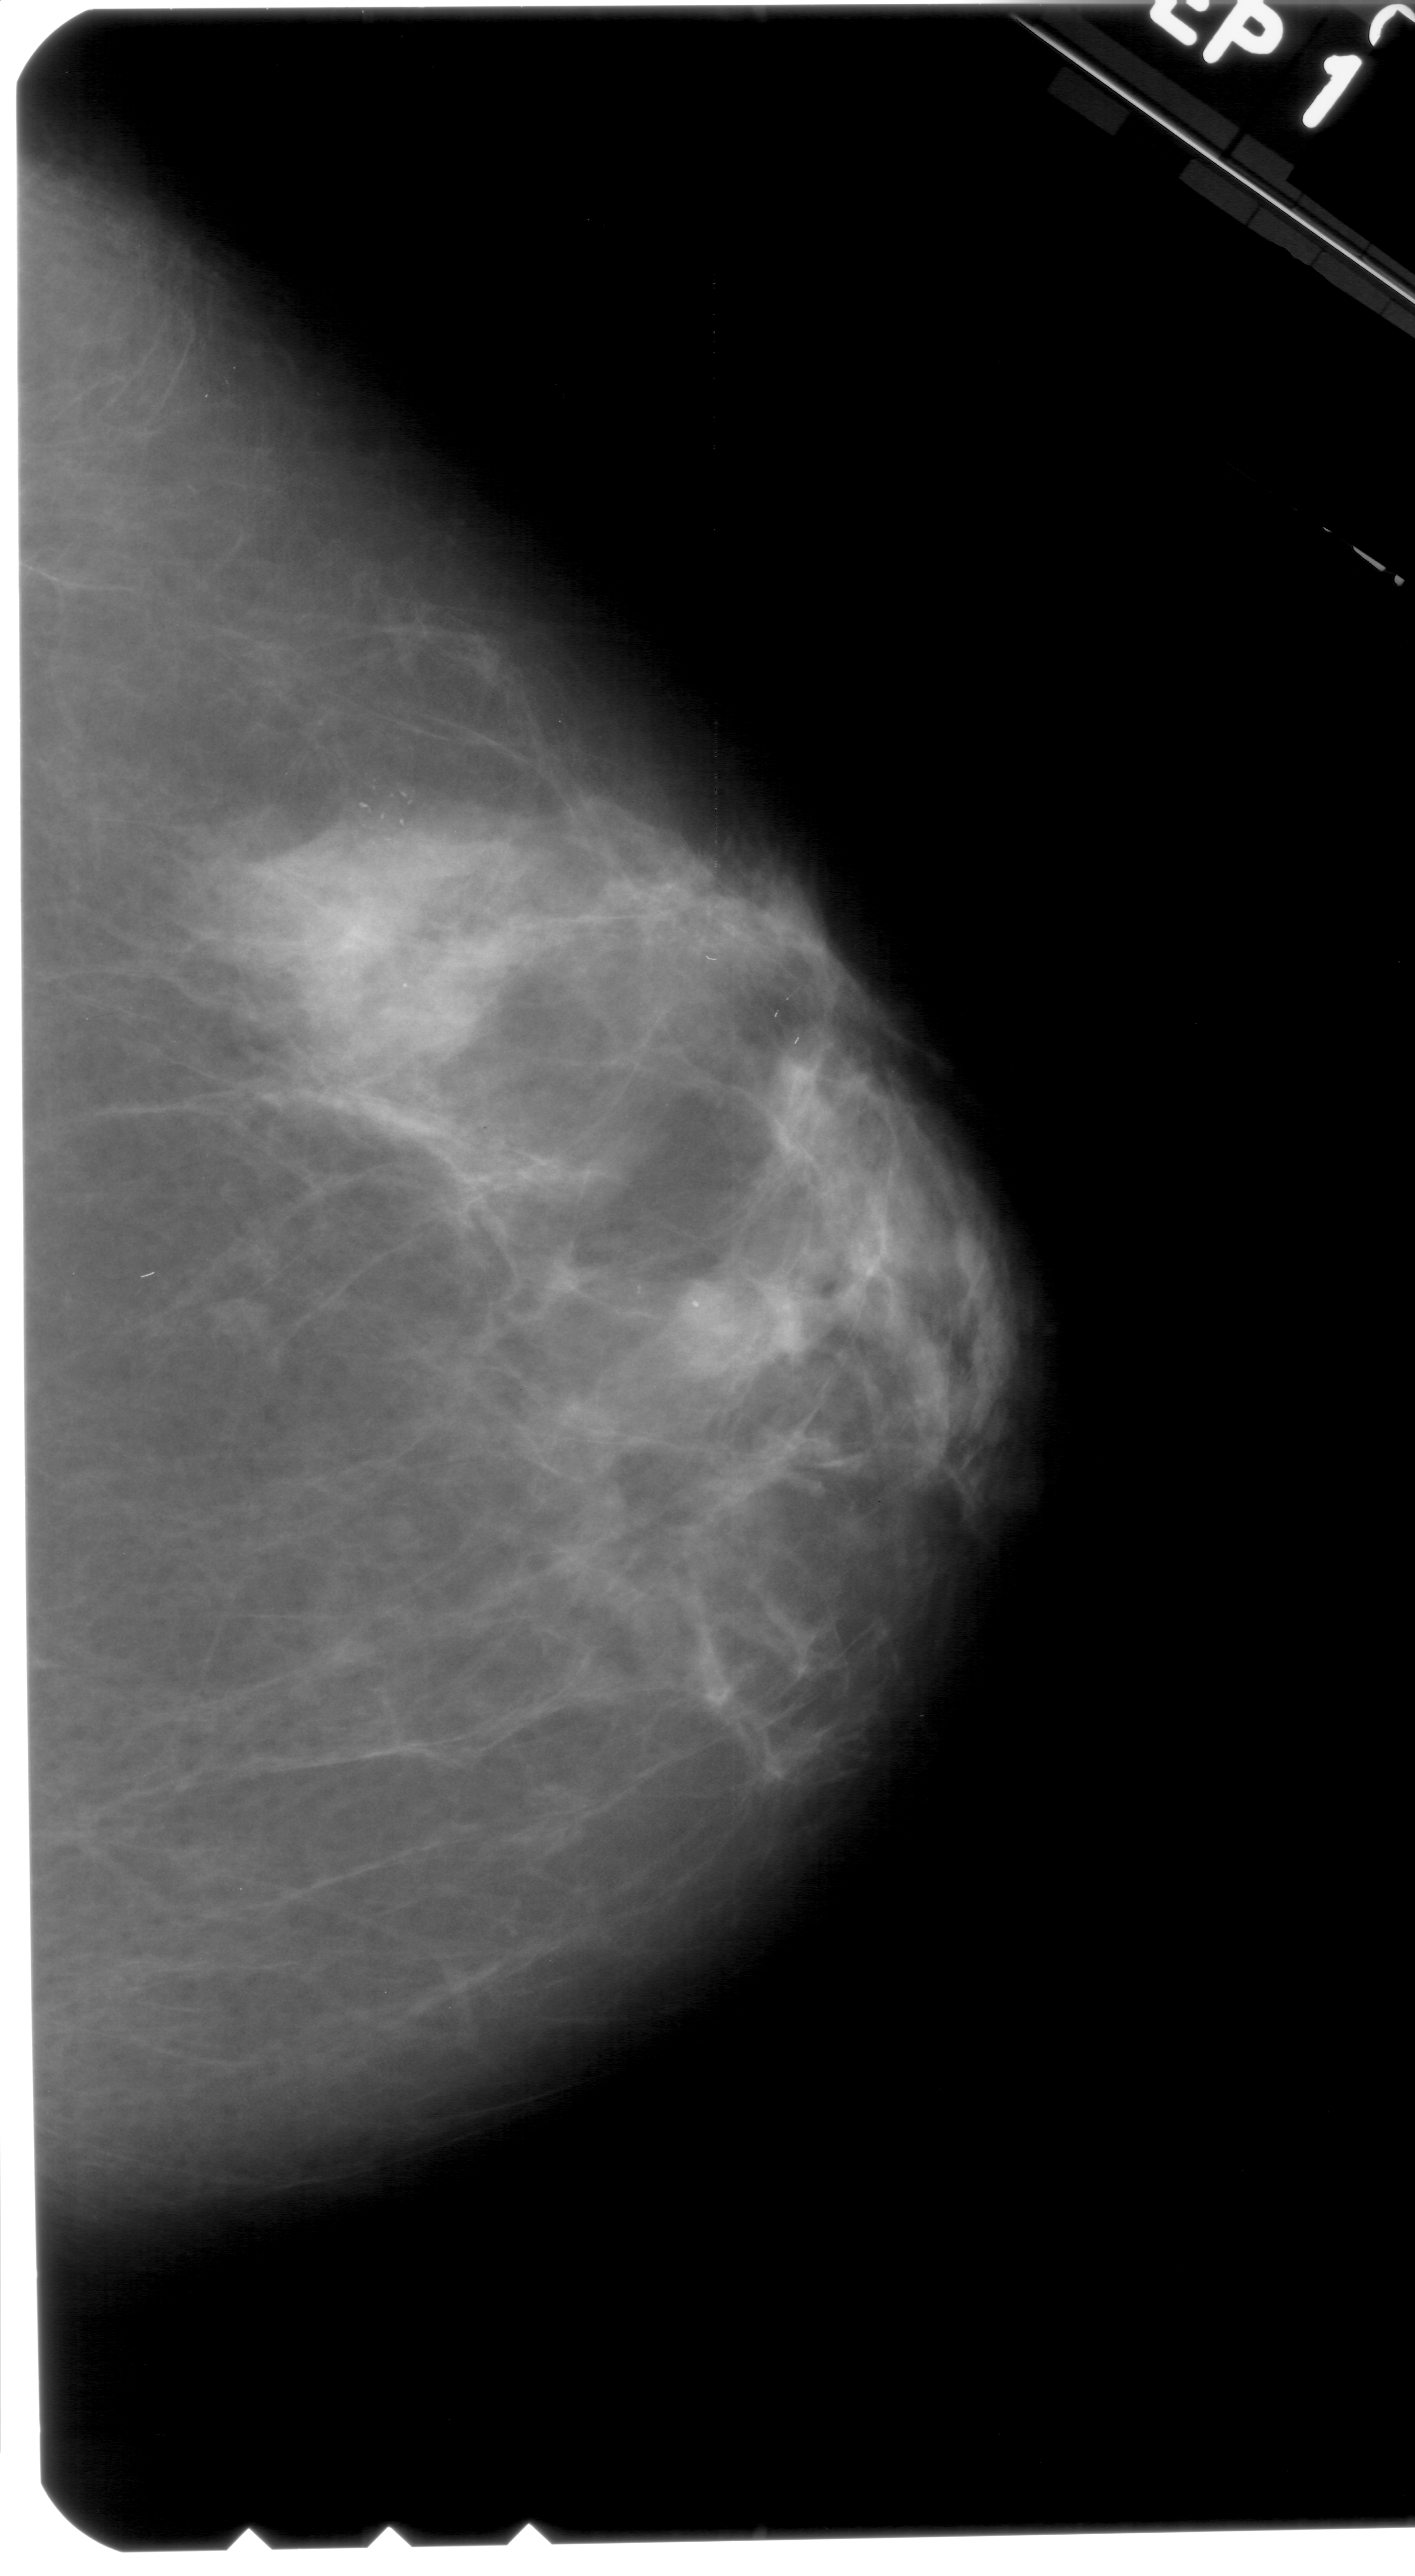
Mammogram (digitized film). Right breast. Craniocaudal (CC) view. Breast composition: extremely dense (BI-RADS density category 4 of 4). 1415 × 2576 image matrix.
Expert-marked regions of interest on this image (one box per marked abnormality):
- calcifications, morphology pleomorphic, distribution clustered; BI-RADS assessment category 4; pathology result (as recorded, not read from the image): benign: bounding box (x1, y1, x2, y2) in pixels: (343, 752, 438, 855)